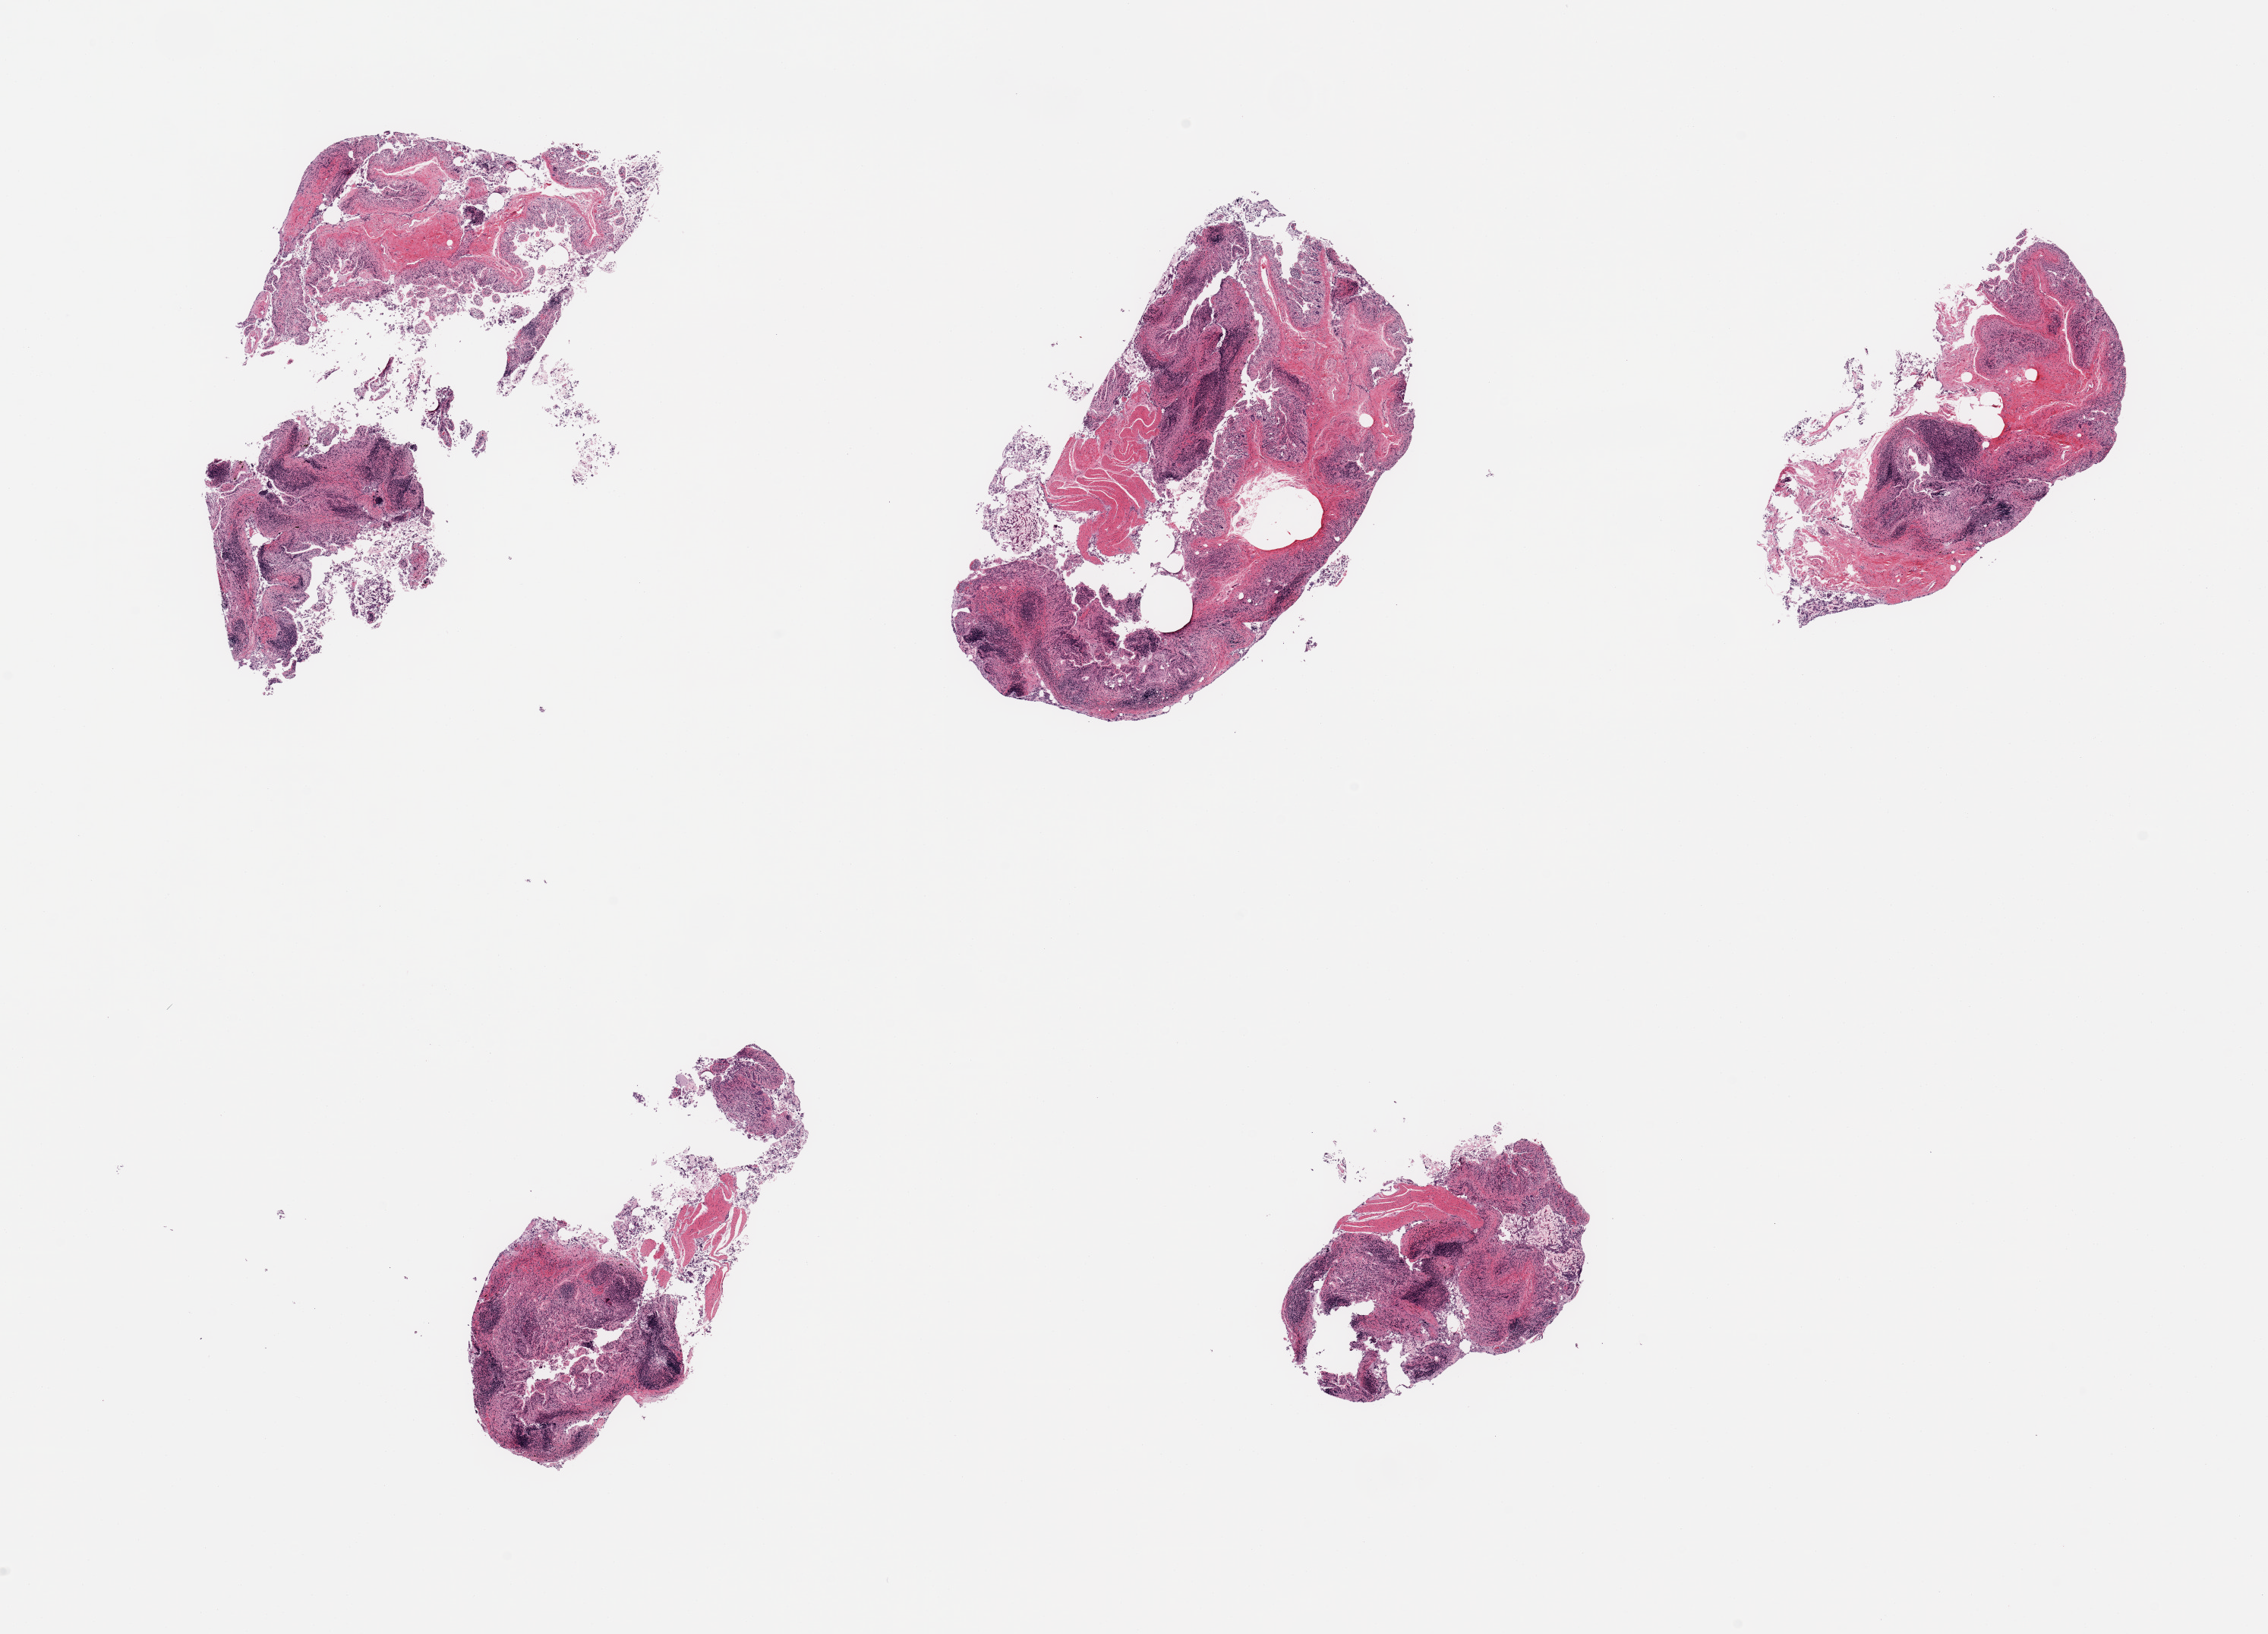
Whole-slide image, hematoxylin and eosin (H&E) stain, brightfield — shown as a low-resolution overview of the whole scanned area (about 23.6 x 17.0 mm). Donor sex: male.
Specimen: PAXgene-fixed paraffin-embedded (PFPE) section; section of ileum (target tissue); tissue donor sample.